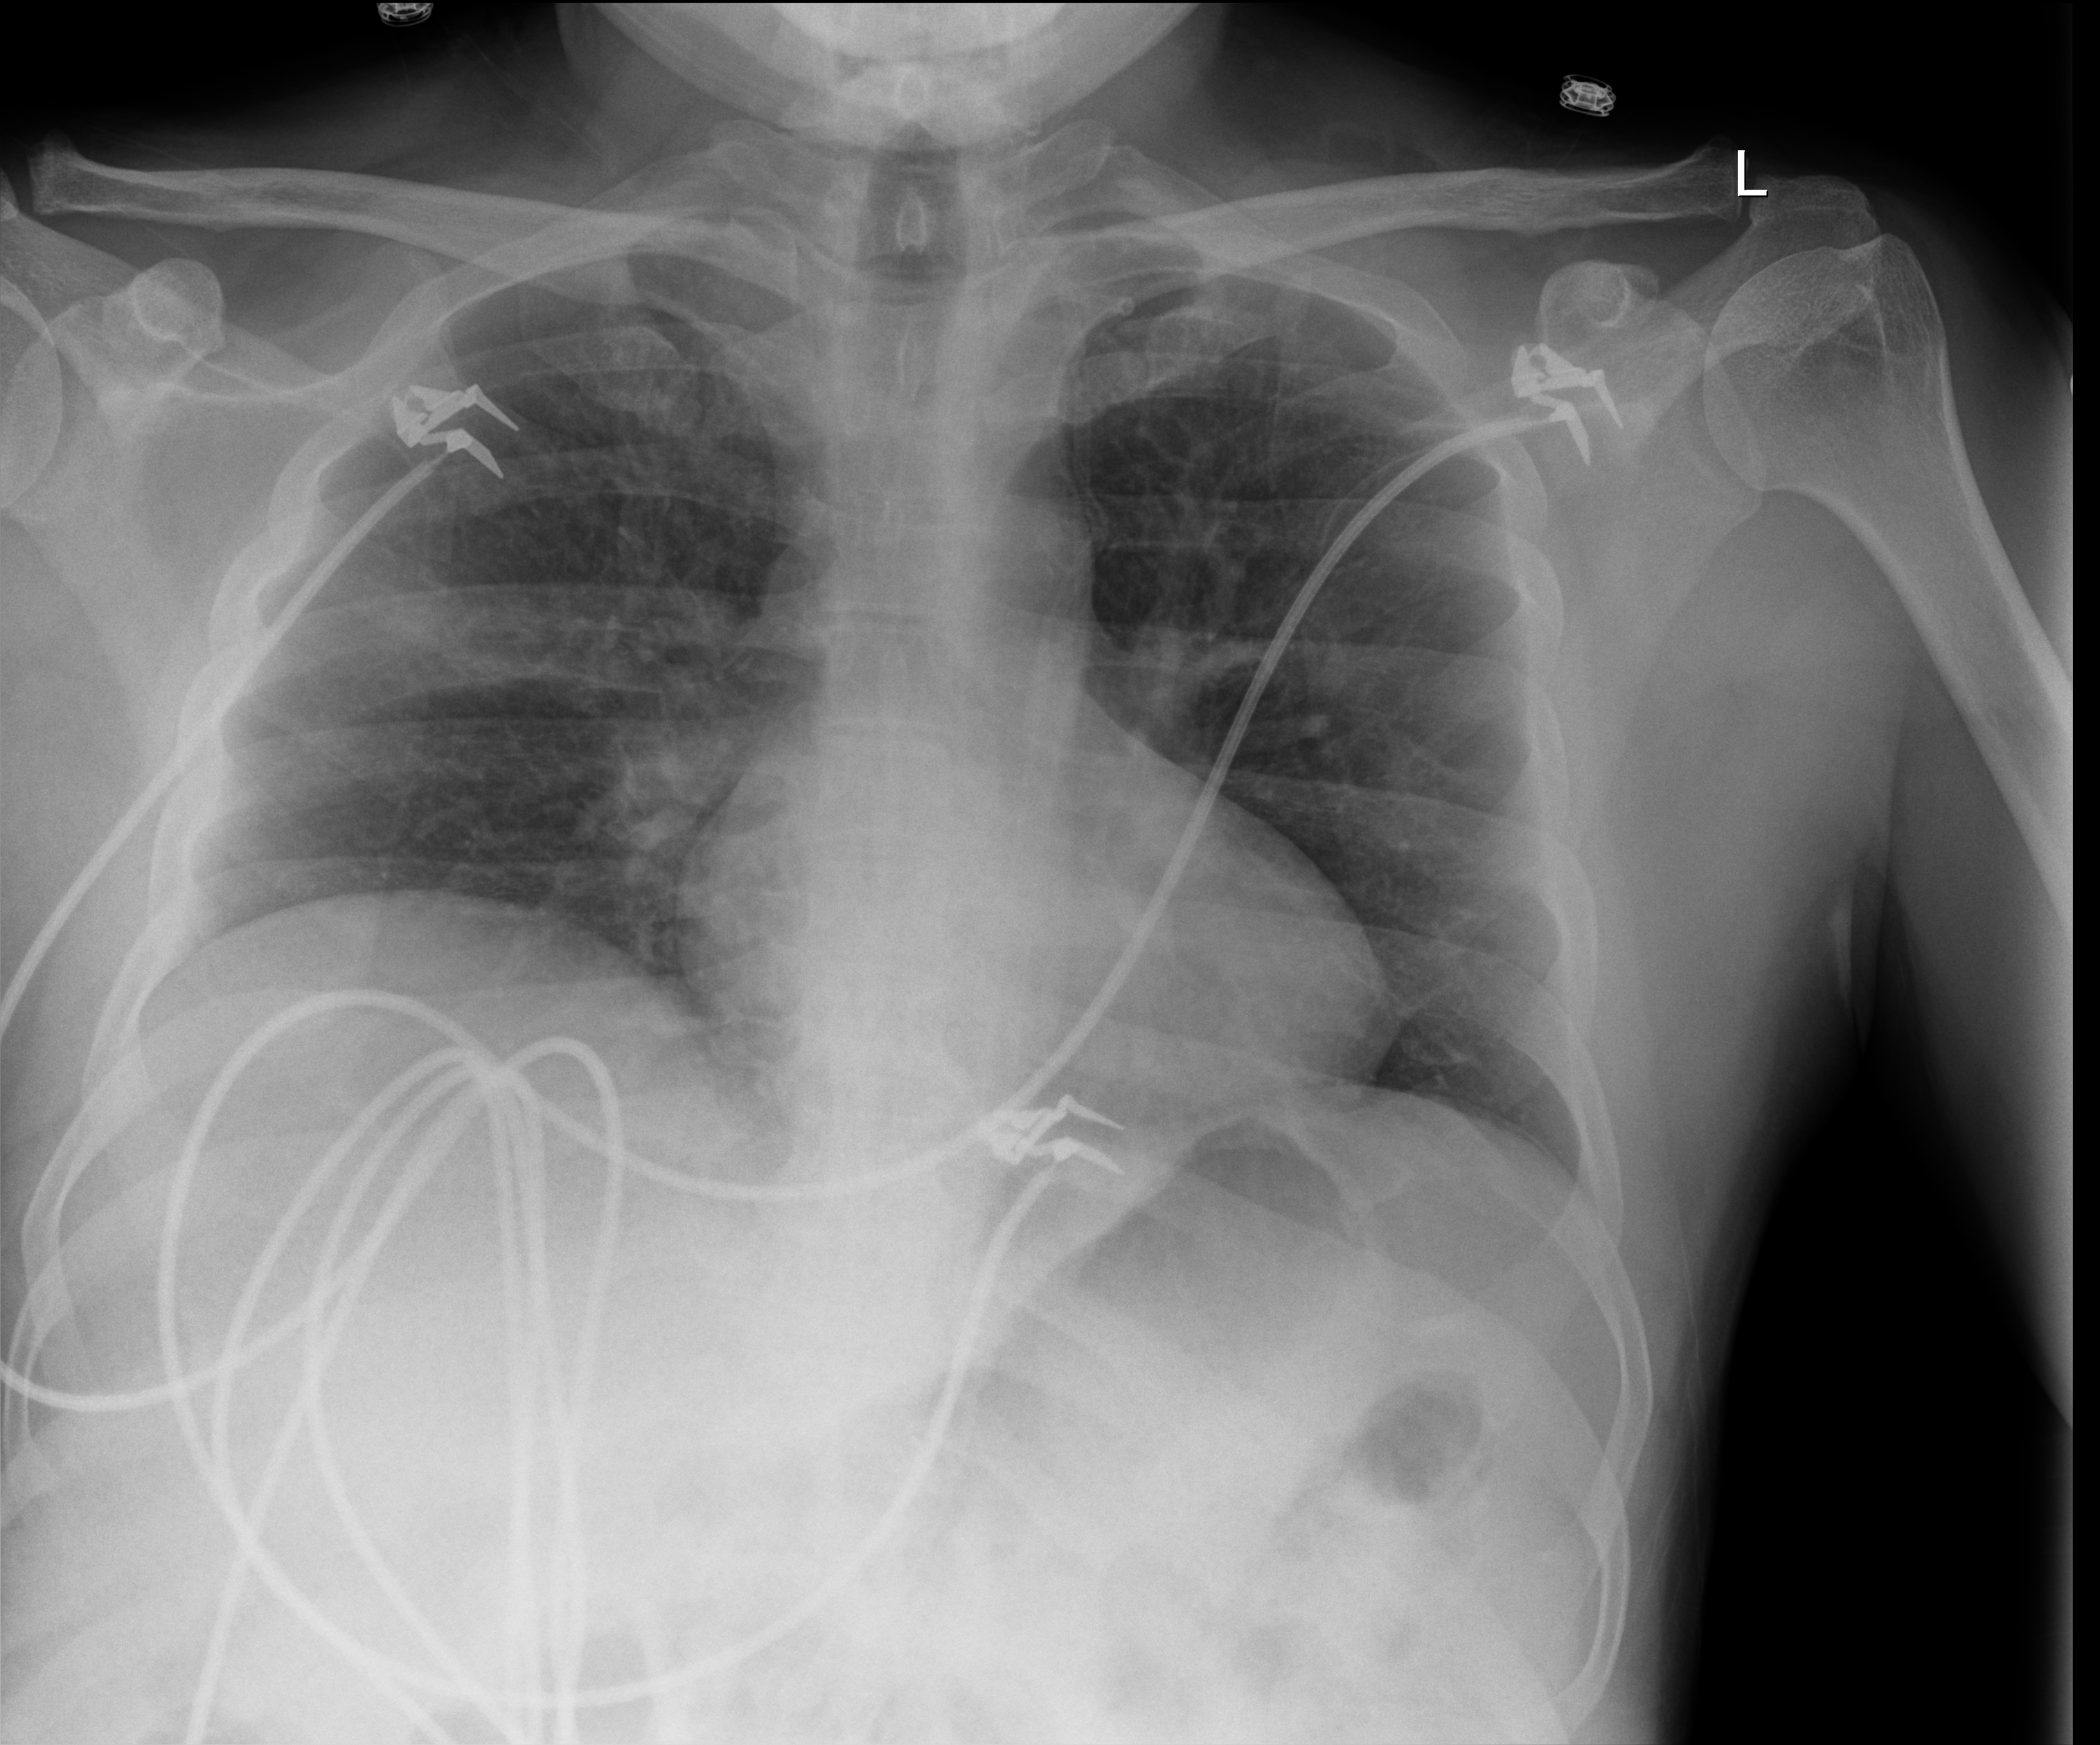
Chest X-ray, anteroposterior (AP) projection. Patient hospitalised with COVID-19, aged 18–59 years.
Hospital-stay facts (about this admission, not read from this image; timing relative to this image not recorded):
- other chronic lung disease (admission record): no
- smoking status (admission record): former
- mechanically ventilated during this hospital stay: no